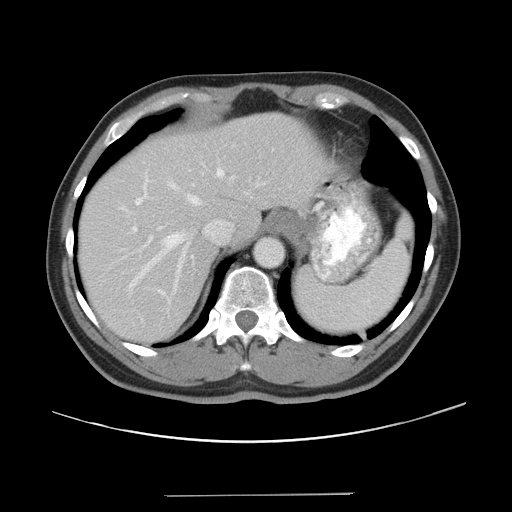
Contrast-enhanced abdominal CT, one axial slice. Position 32 of 43 along the scan axis. Intravenous contrast given. Soft-tissue window (W 400 / L 40 HU). 5 mm slice thickness. 512 × 512 image matrix, field of view 409 × 409 mm. Male patient, age 65 years. From the clinical record (not read from this slice): diagnosis: colorectal cancer liver metastases, imaged before liver resection; multiple liver metastases: no; largest metastasis: 3.8 cm; disease in both lobes: no.
Annotated regions visible in this slice (outlined manually by an expert reader):
- hepatic veins: bounding box (x1, y1, x2, y2) in pixels: (140, 170, 224, 294)
- liver: (79, 115, 319, 341)
- planned liver remnant (the part of the liver to remain after resection): (79, 115, 319, 336)
- portal vein (with intrahepatic branches): (132, 186, 147, 232)